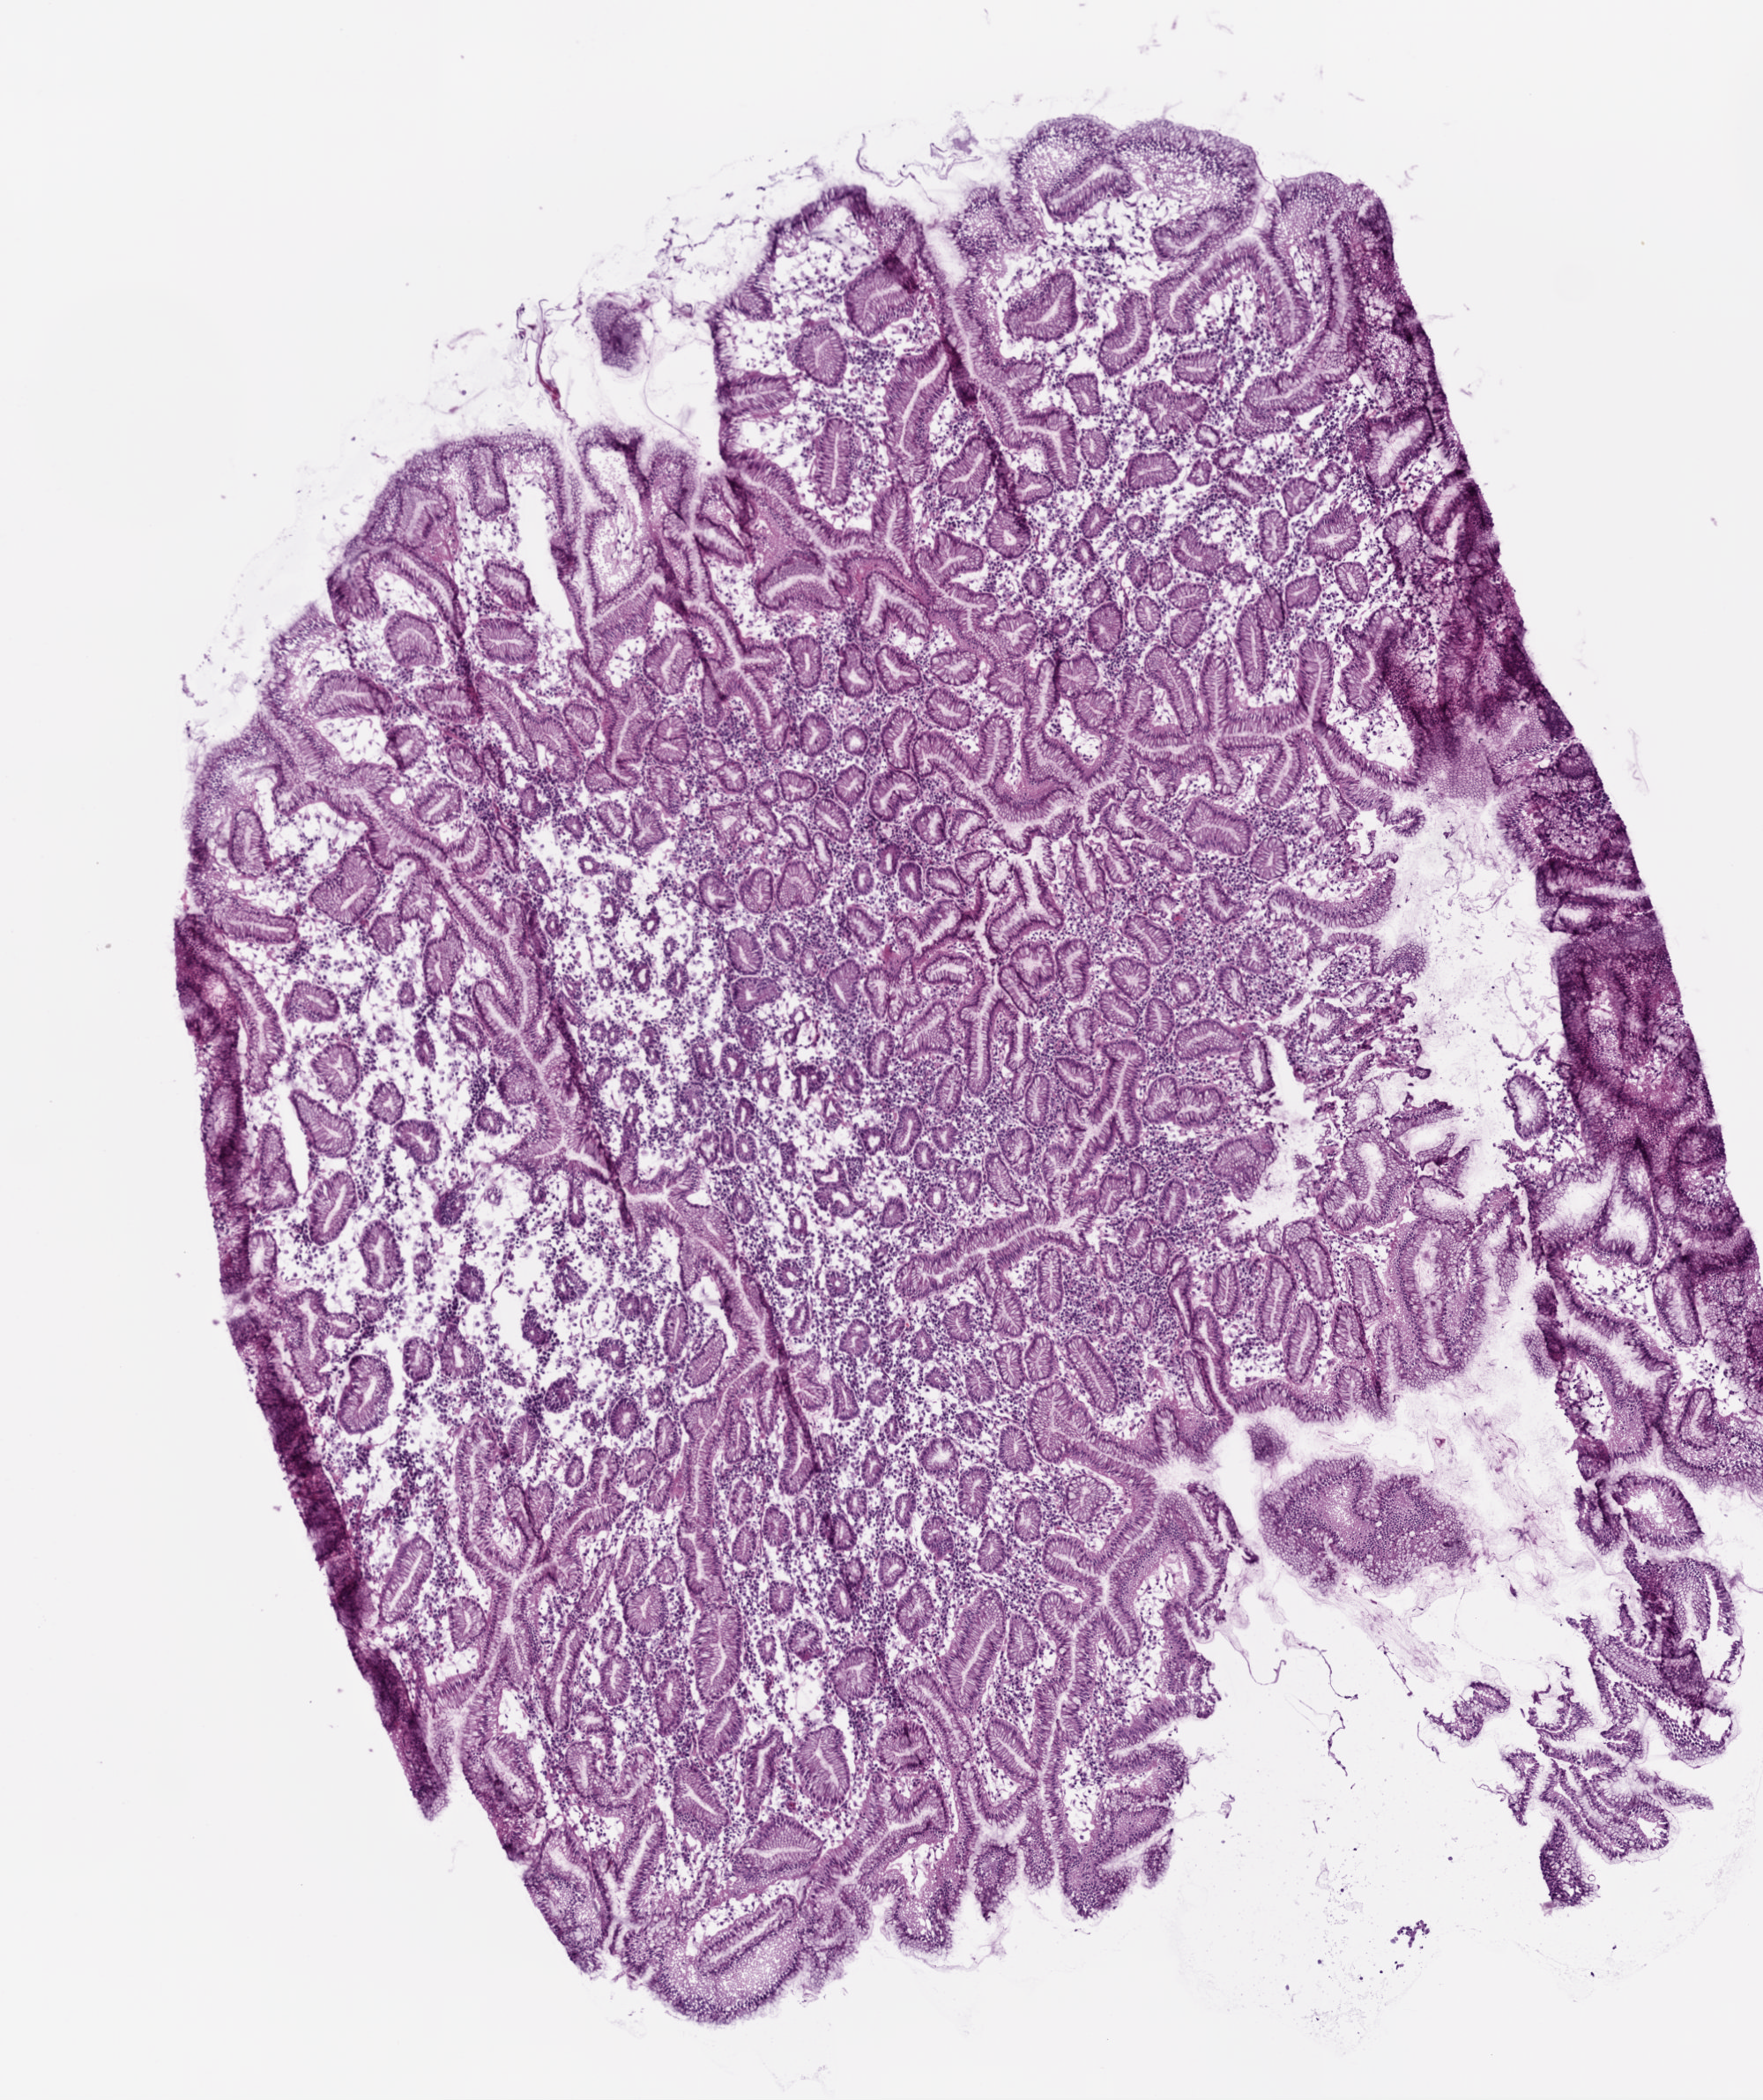
Whole-slide histology image, H&E-stained, a low-resolution overview of the entire scanned area, about 4.0 x 4.8 mm (slide scanned at 20x). Frozen section from the top of the tissue portion. Stomach, solid tissue normal (non-tumour tissue) sample. Female, age 83 years at initial diagnosis.
This section: solid tissue normal sample (biorepository sample class). Patient diagnosis: Adenocarcinoma, intestinal type (gastric antrum).